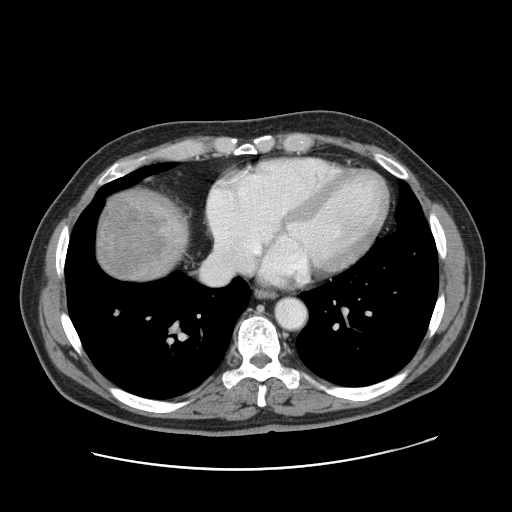
Contrast-enhanced abdominal CT, one axial slice; position 158 of 178 along the scan axis; 120 kVp; intravenous contrast given; soft-tissue window (W 400 / L 40 HU); 2.5 mm slice thickness; 512 × 512 image matrix, field of view 403 × 403 mm. Male patient, age 63 years. Case-level facts recorded for this patient, not image findings: diagnosis: colorectal cancer liver metastases, imaged before liver resection; multiple liver metastases: yes; largest metastasis: 8 cm; disease in both lobes: yes.
Annotated regions visible in this slice (expert manual segmentation):
- liver: bounding box [x1, y1, x2, y2] px = [95, 191, 190, 282]
- liver metastasis: [98, 193, 166, 278]